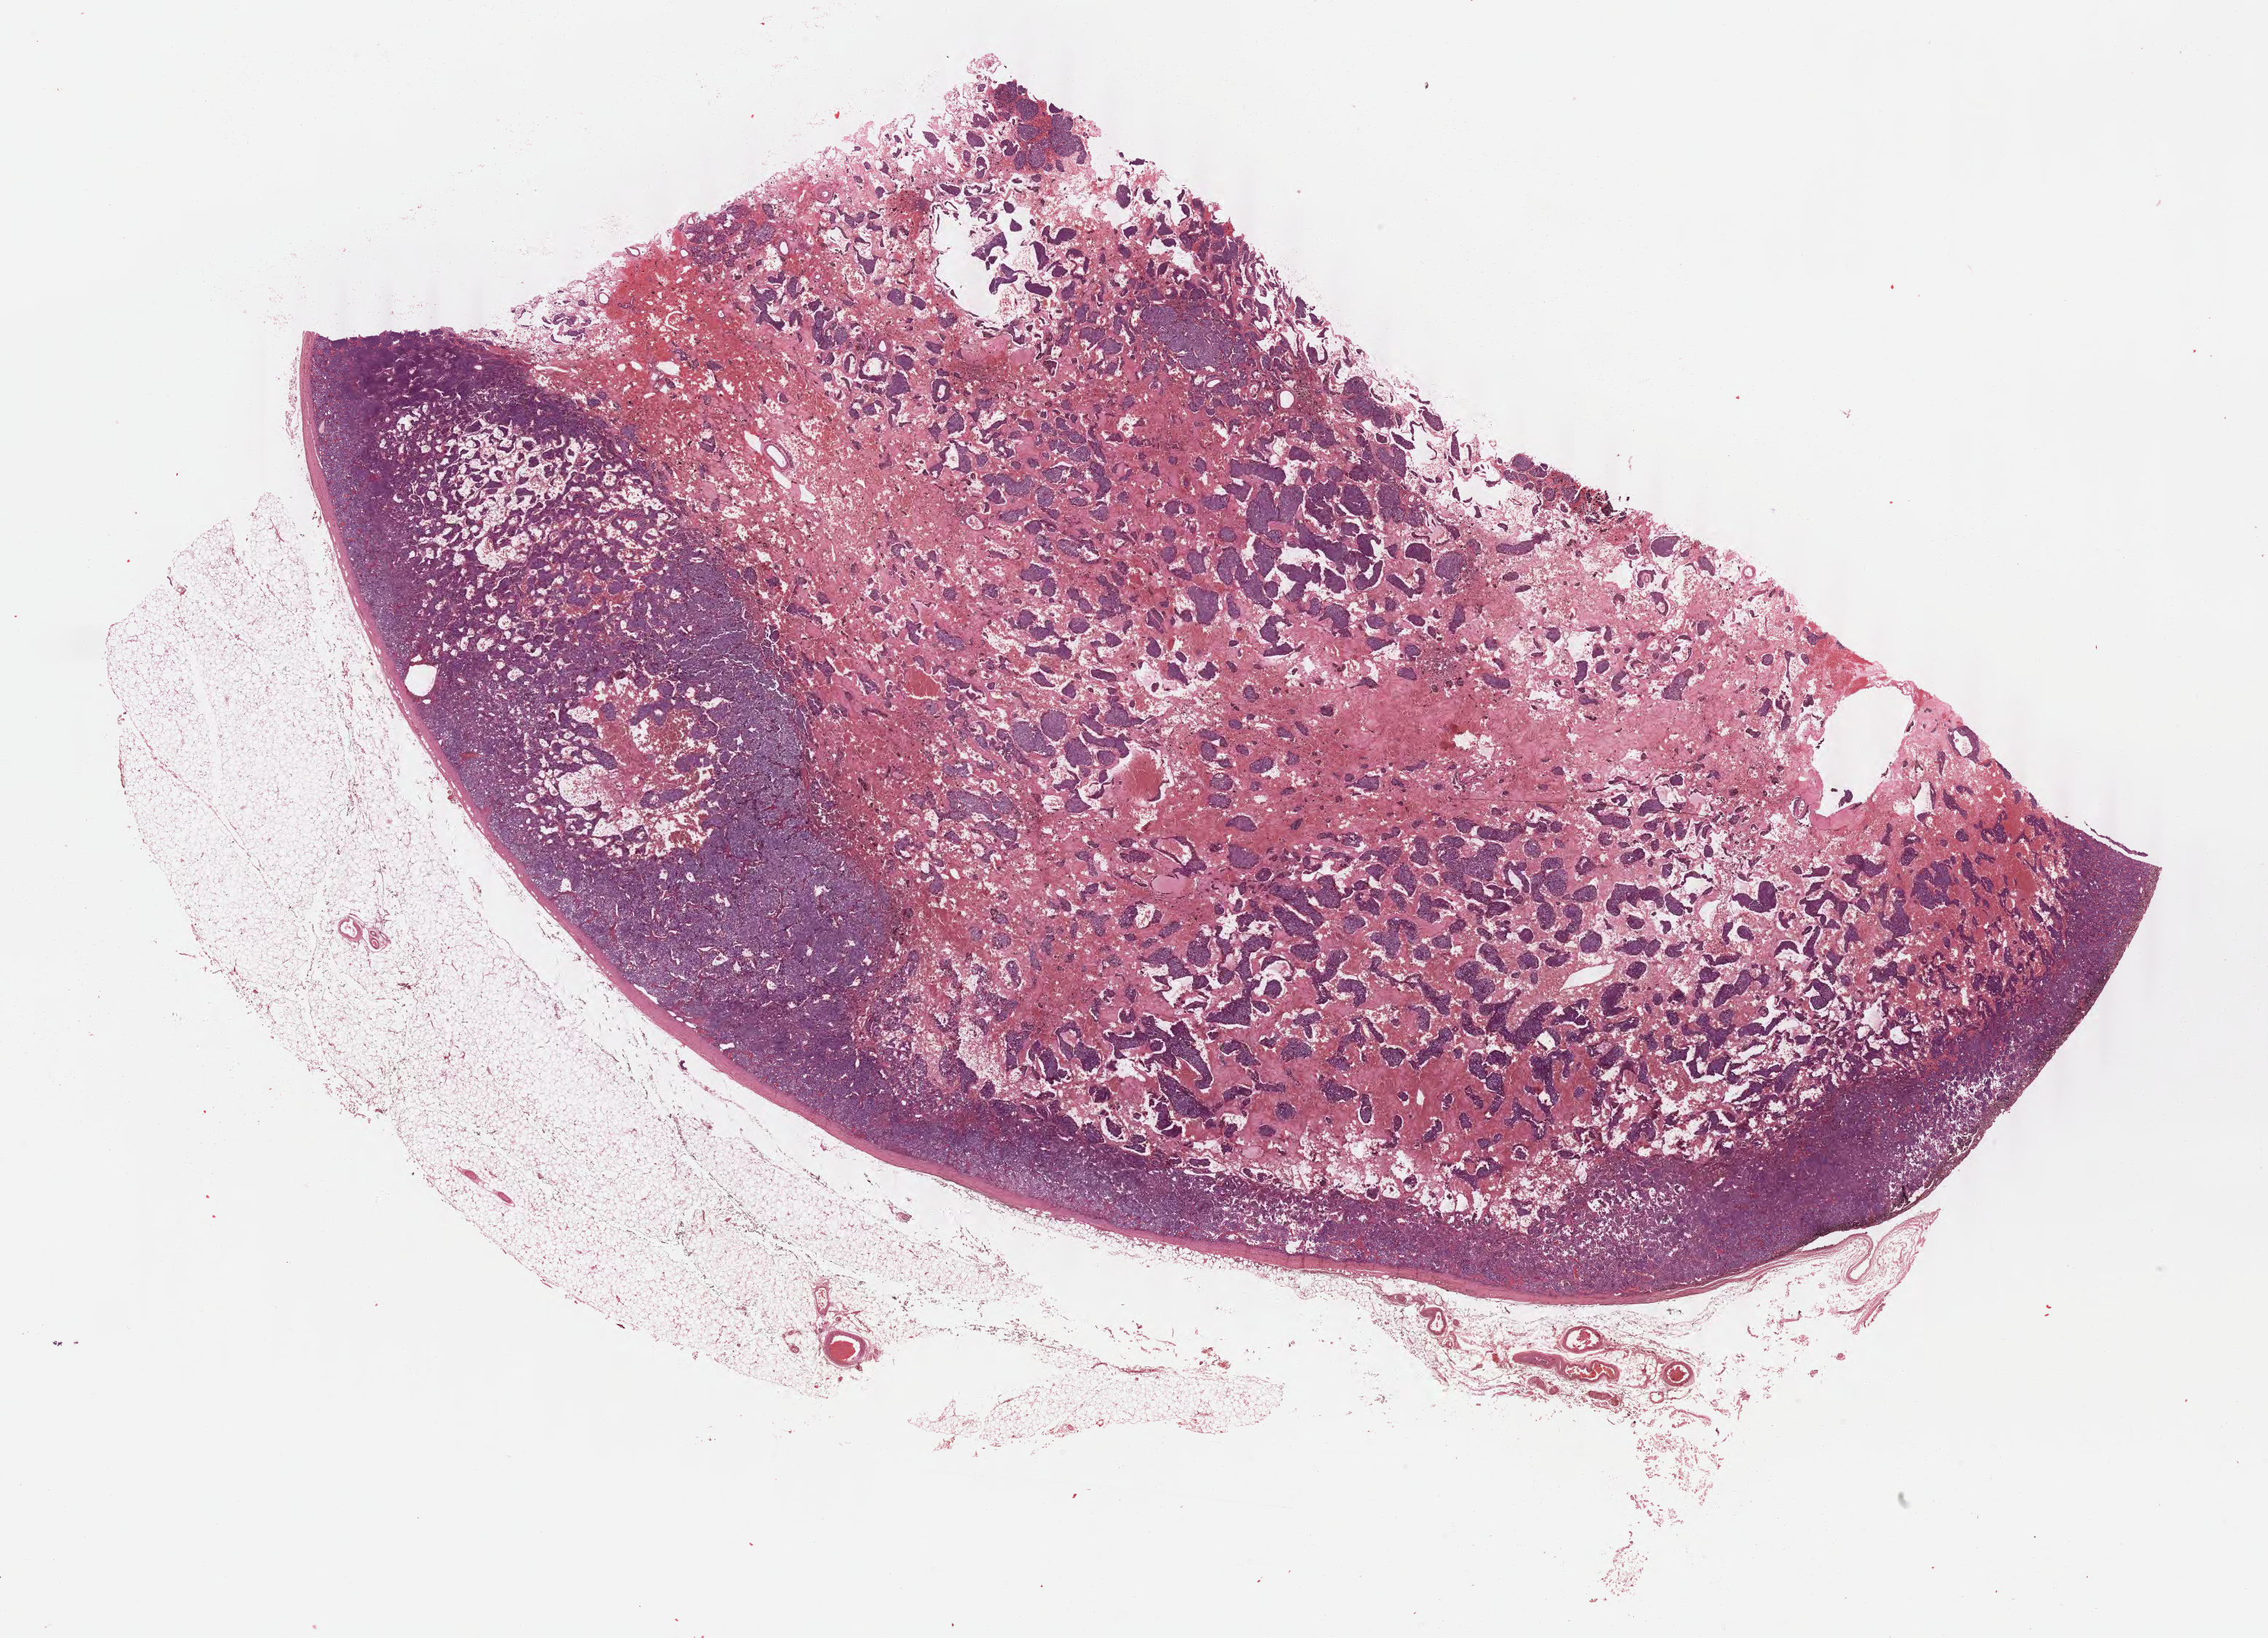
H&E whole-slide image — a low-resolution overview of the entire scanned area, about 24.6 x 17.8 mm. Formalin-fixed paraffin-embedded (FFPE) diagnostic section. Primary tumour sample from the adrenal gland. Patient: male, age at initial diagnosis 46 years.
• histologic diagnosis: Pheochromocytoma, NOS